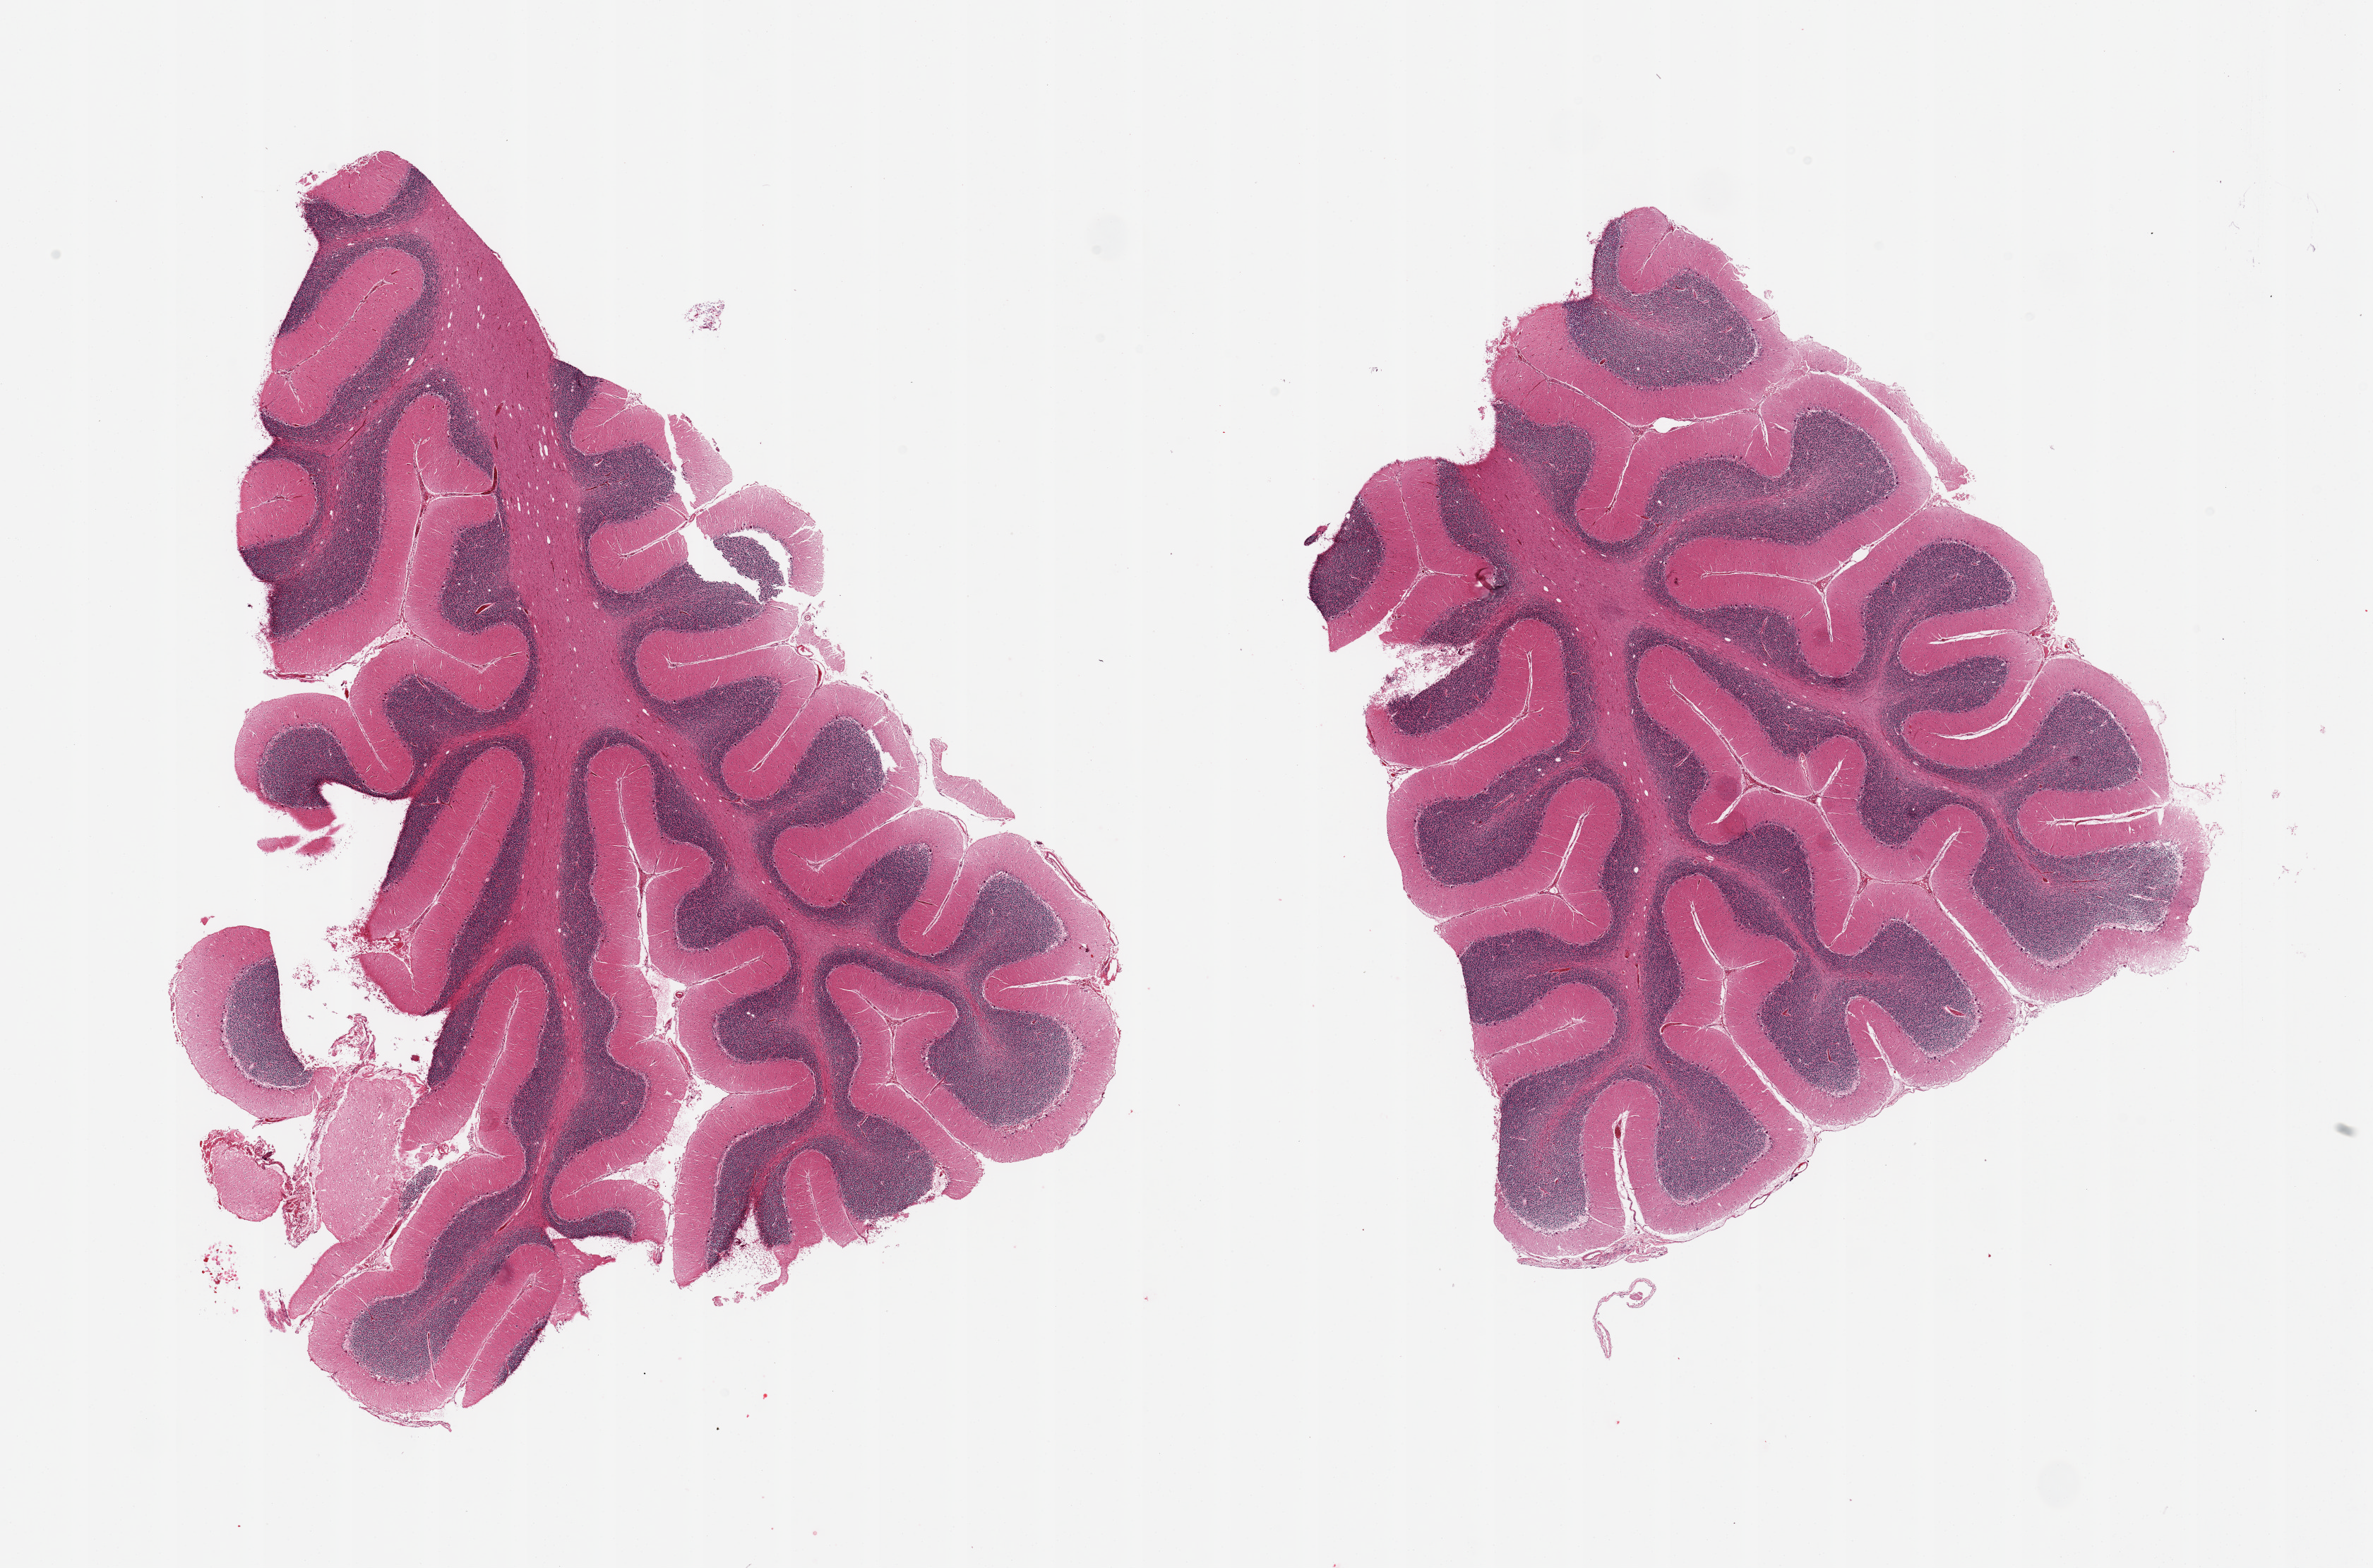
Digitized haematoxylin and eosin-stained section, brightfield, shown as a low-resolution overview of the whole scanned area (about 26.6 x 17.6 mm, slide scanned at 20x), PAXgene-fixed paraffin-embedded (PFPE) section, target tissue: cerebellum, donor tissue sample. Donor: male.
Reviewer comment on this tissue sample: 2 pieces, no abnormalities.